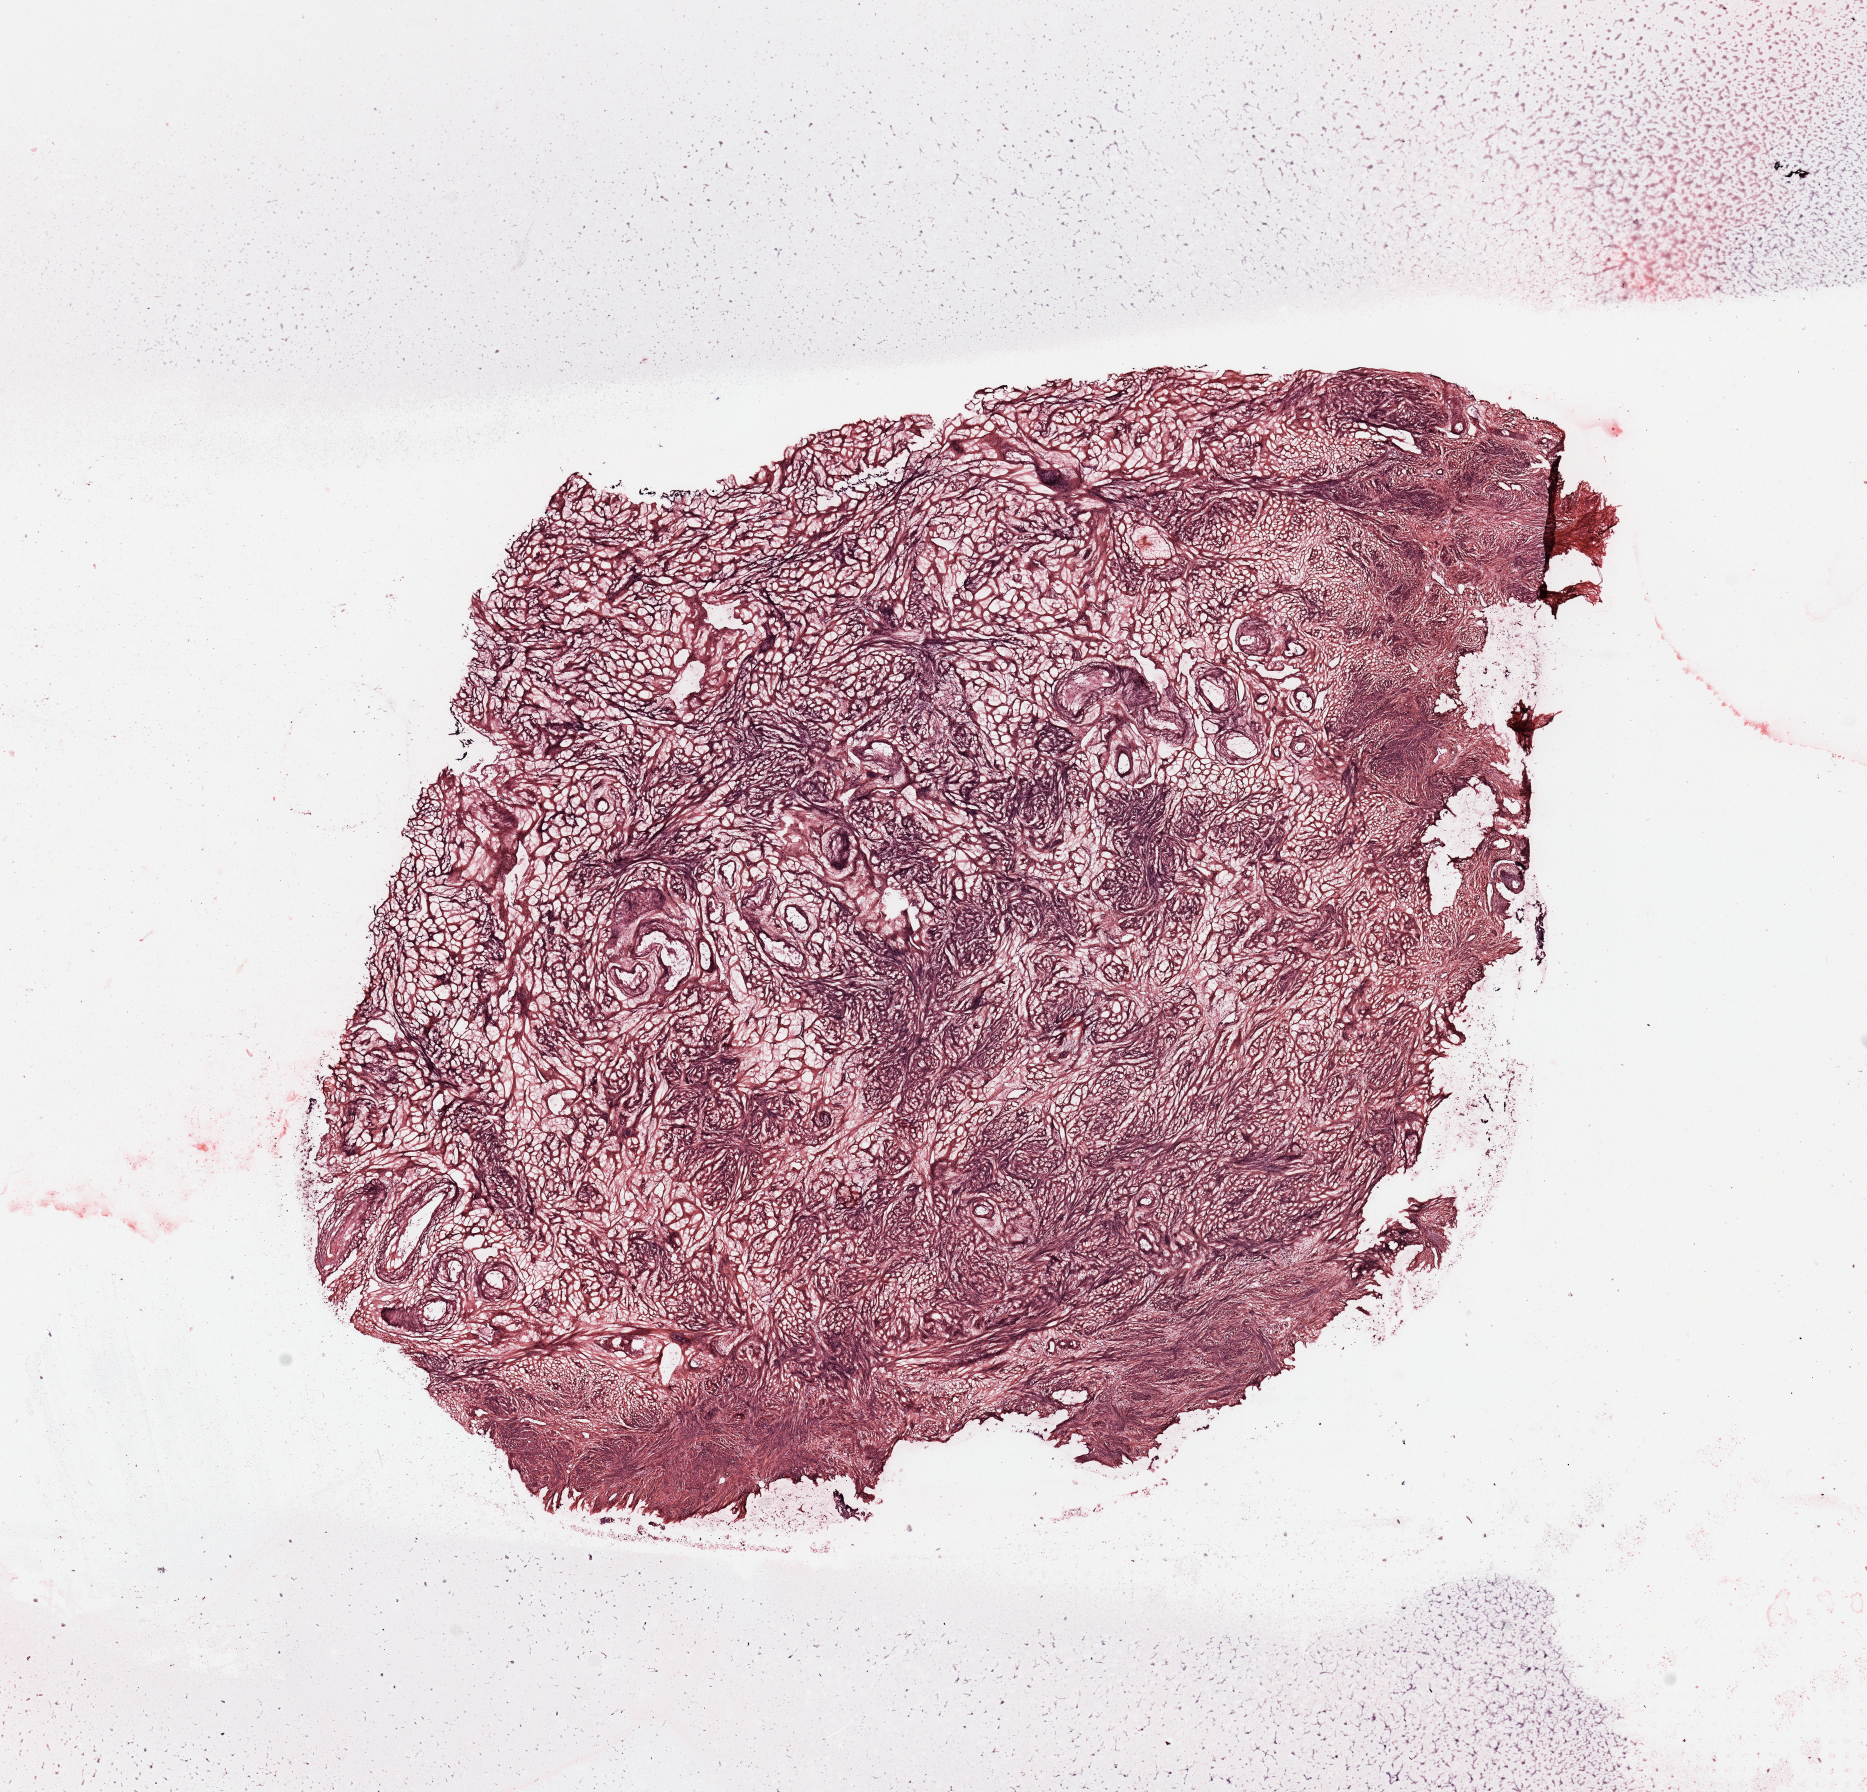
H&E whole-slide image, whole scanned area (about 14.8 x 14.2 mm, acquisition: 20x scan) shown as a low-resolution overview; uterus, normal (non-tumour) tissue. 64-year-old female patient.
This section: normal (non-tumour) tissue from the same patient. Patient diagnosis: Endometrioid adenocarcinoma, NOS.